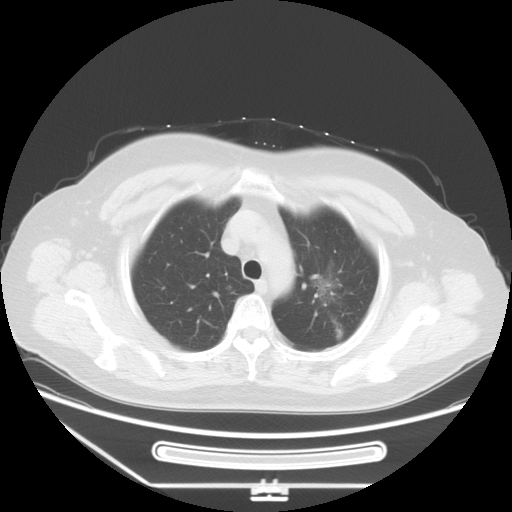
Chest CT, one axial slice; slice 44 of 53 in the series (ordered by position); reconstruction kernel STANDARD; 120 kVp; lung window (W 1500 / L -600 HU); 512 × 512 image matrix. Female patient, age 66 years. Case-level facts recorded for this patient, not image findings: clinical TNM (as recorded): T2 N0 M0; histopathological grade: G2.
Annotated regions visible in this slice (bounding box drawn by a radiologist):
- lung tumour (recorded histology: adenocarcinoma): bounding box [x1, y1, x2, y2] px = [302, 260, 356, 316]